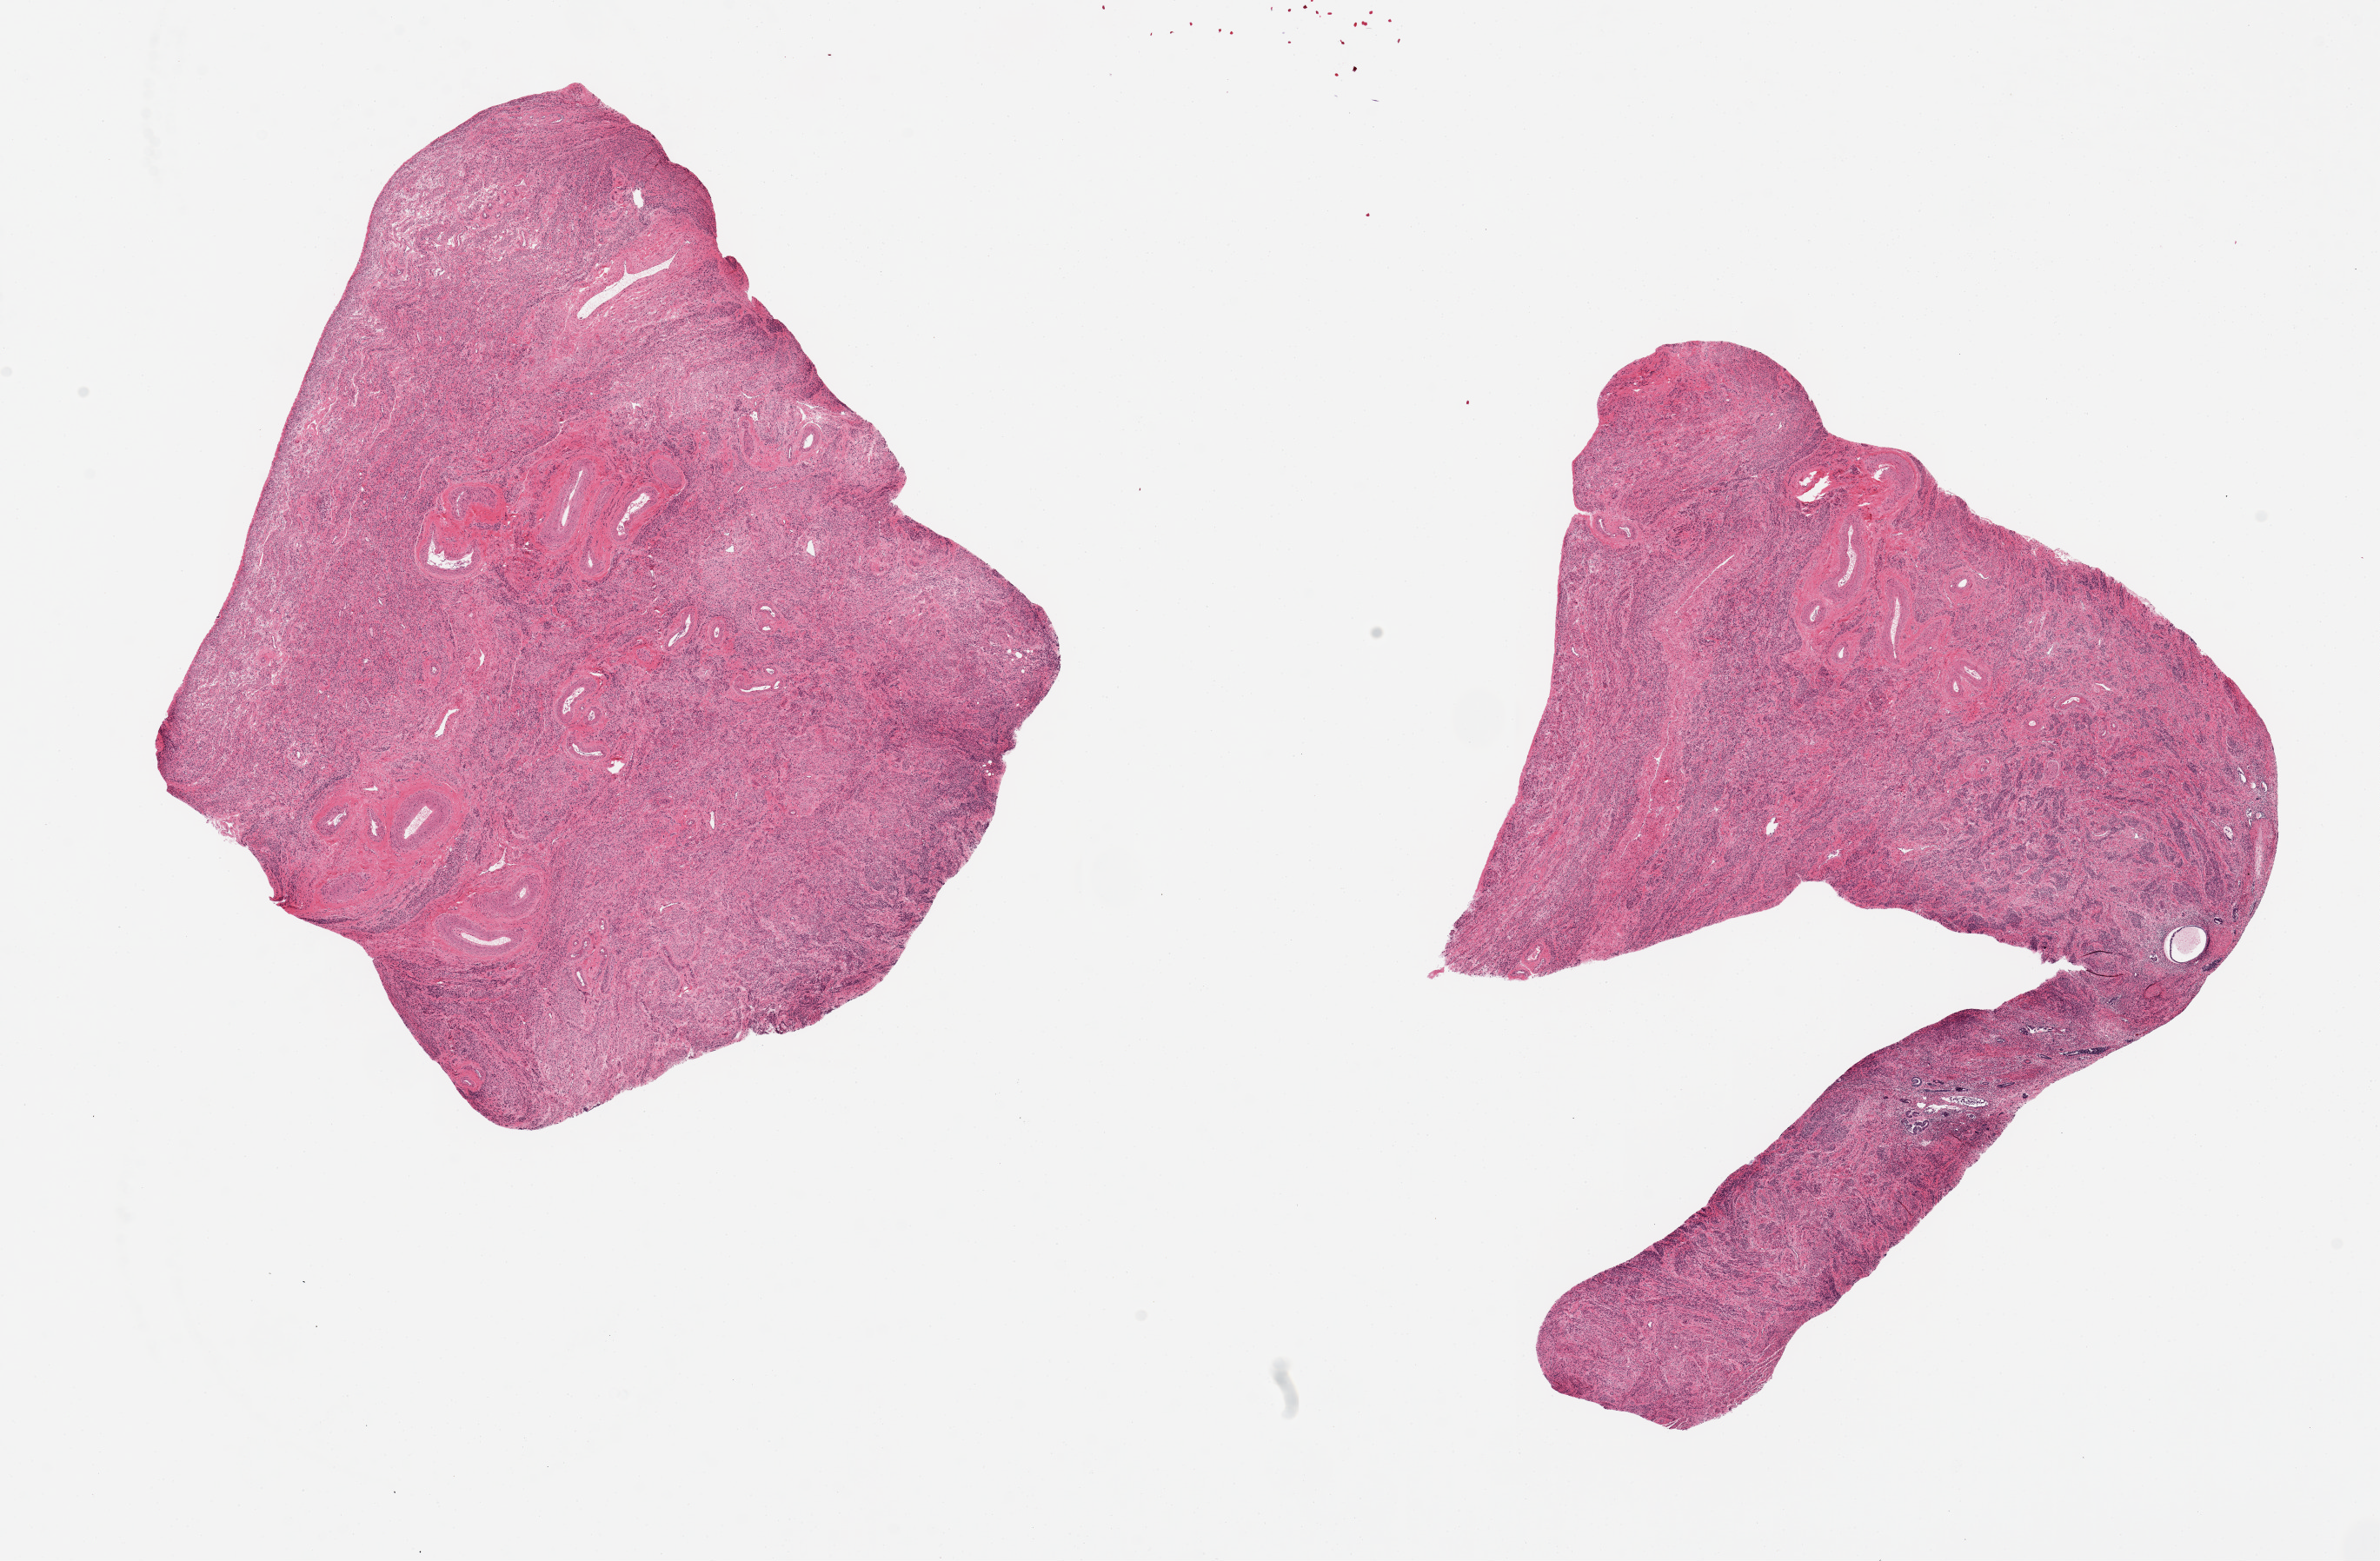
Digitized hematoxylin and eosin (H&E)-stained section, brightfield — shown as a low-resolution overview of the whole scanned area (about 21.7 x 14.2 mm, slide scanned at 20x), PAXgene-fixed, paraffin-embedded tissue, target tissue: uterus, donor tissue sample. Donor: female.
- reviewer comment on this tissue sample: 2 pieces; 8x7 & 9x8mm; glands=2; muscle = 1; small focus of glands in 1 piece